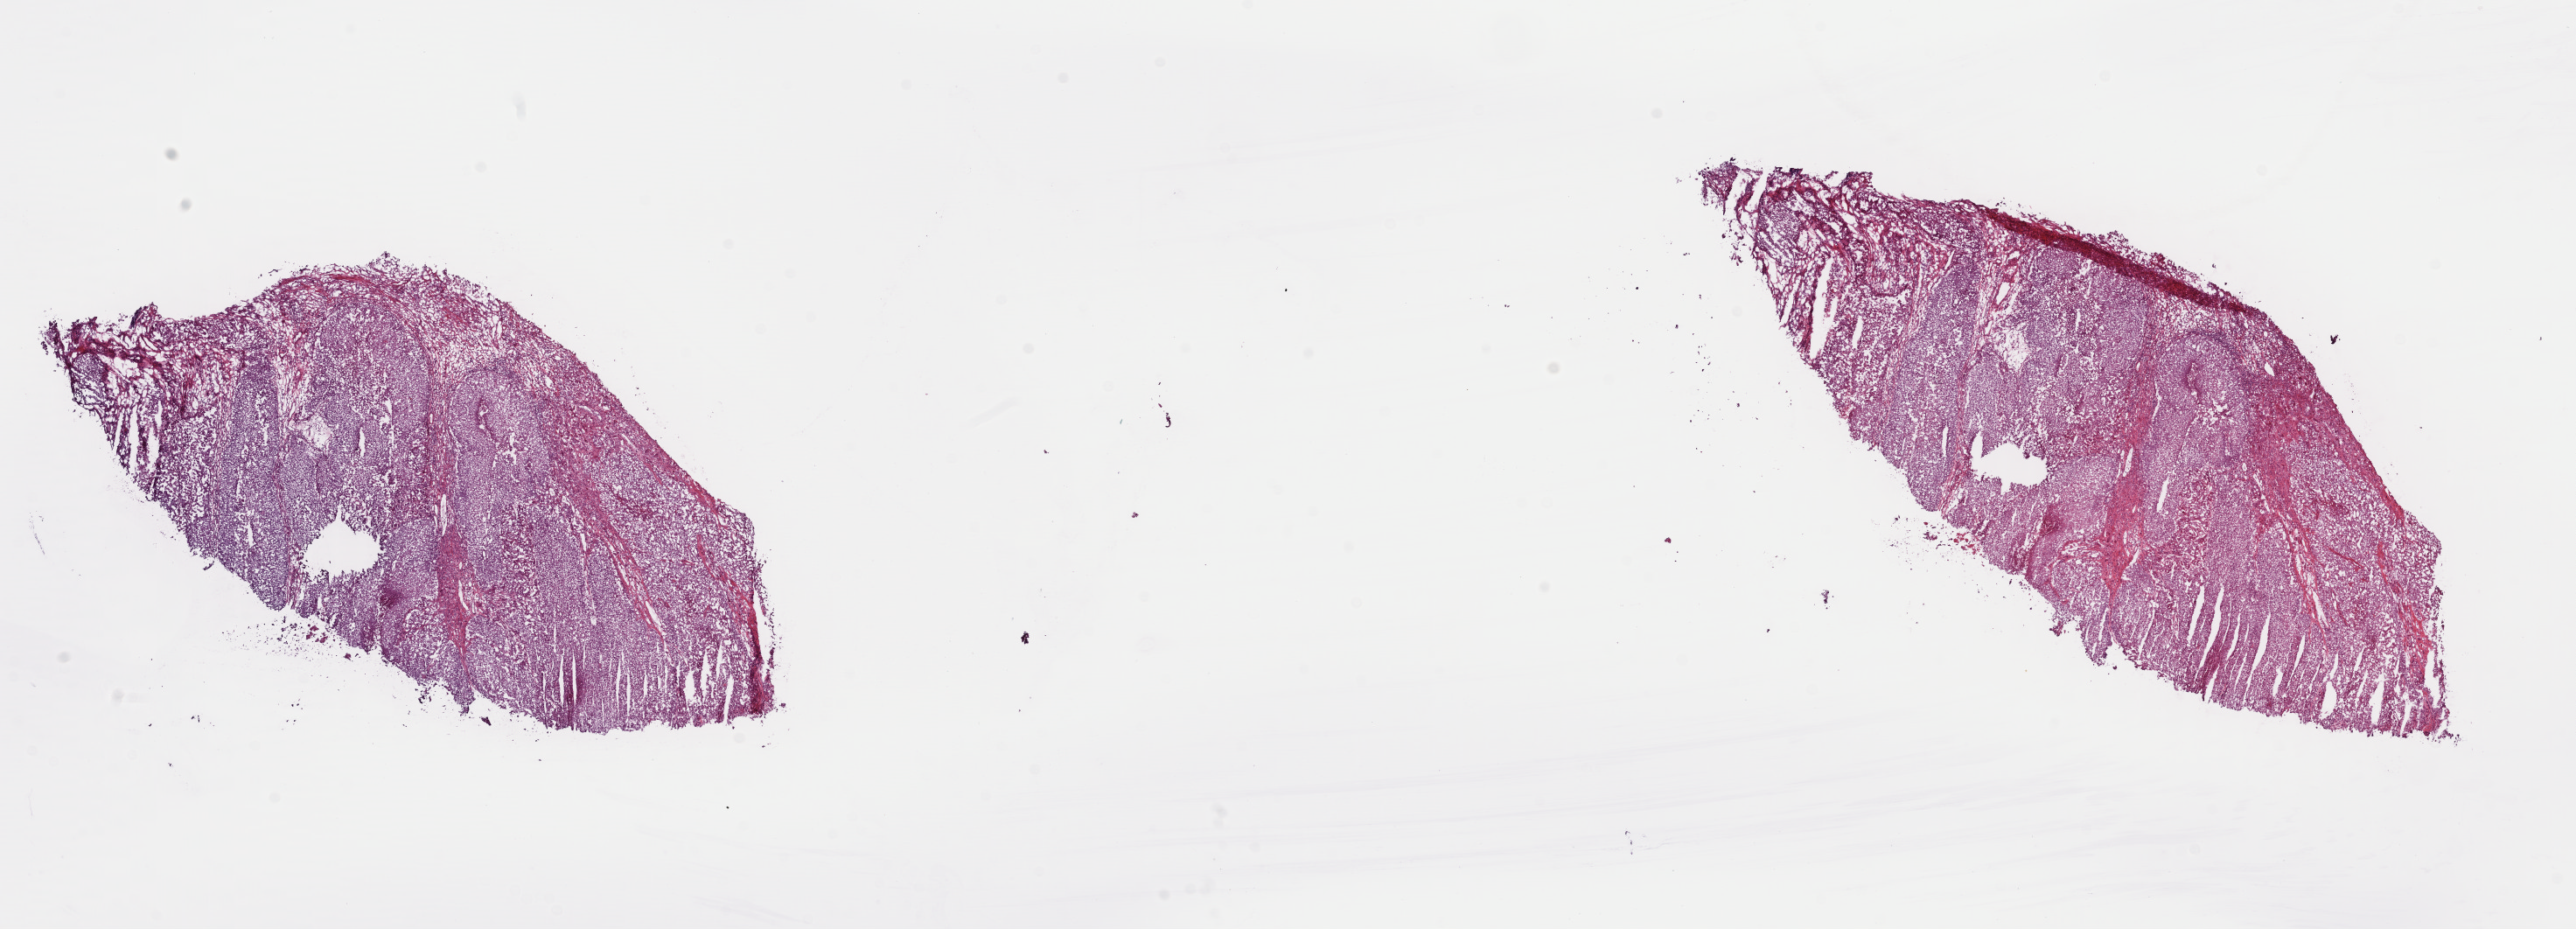
Whole-slide histology image, H&E — a low-resolution overview of the entire scanned area, about 23.2 x 8.4 mm; frozen section from the top of the tissue portion; sample: primary tumour, bladder. Patient: male, age at initial diagnosis 66 years. Histologic grade: high grade. Slide review estimates, as recorded: tumour cells 85%, tumour nuclei 80%, normal cells 0%, stromal cells 15%, necrosis 0%. Infiltration values recorded for this section: lymphocyte infiltration 0%, monocyte infiltration 0%, neutrophil infiltration 0%.
TNM: T2 N0 M0. Histologic diagnosis: Transitional cell carcinoma. AJCC pathologic stage: II.